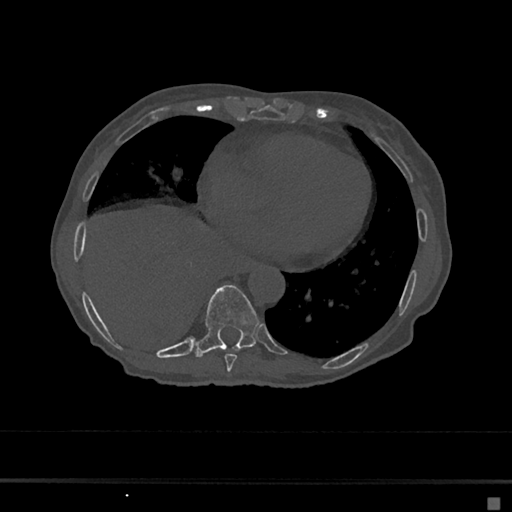
CT including the spine, one axial slice. Slice 288 of 797 in the series (ordered by position). Reconstruction kernel Br40s/3. Bone window (W 1800 / L 400 HU). 512 × 512 image matrix, field of view 360 × 360 mm. Female patient, age 68 years. Case-level facts recorded for this patient, not image findings: primary cancer: renal.
Annotated regions visible in this slice (semi-automatically segmented with operator editing):
- T8 vertebra: bounding box [x1, y1, x2, y2] px = [224, 354, 237, 372]
- T9 vertebra: [196, 285, 260, 357]